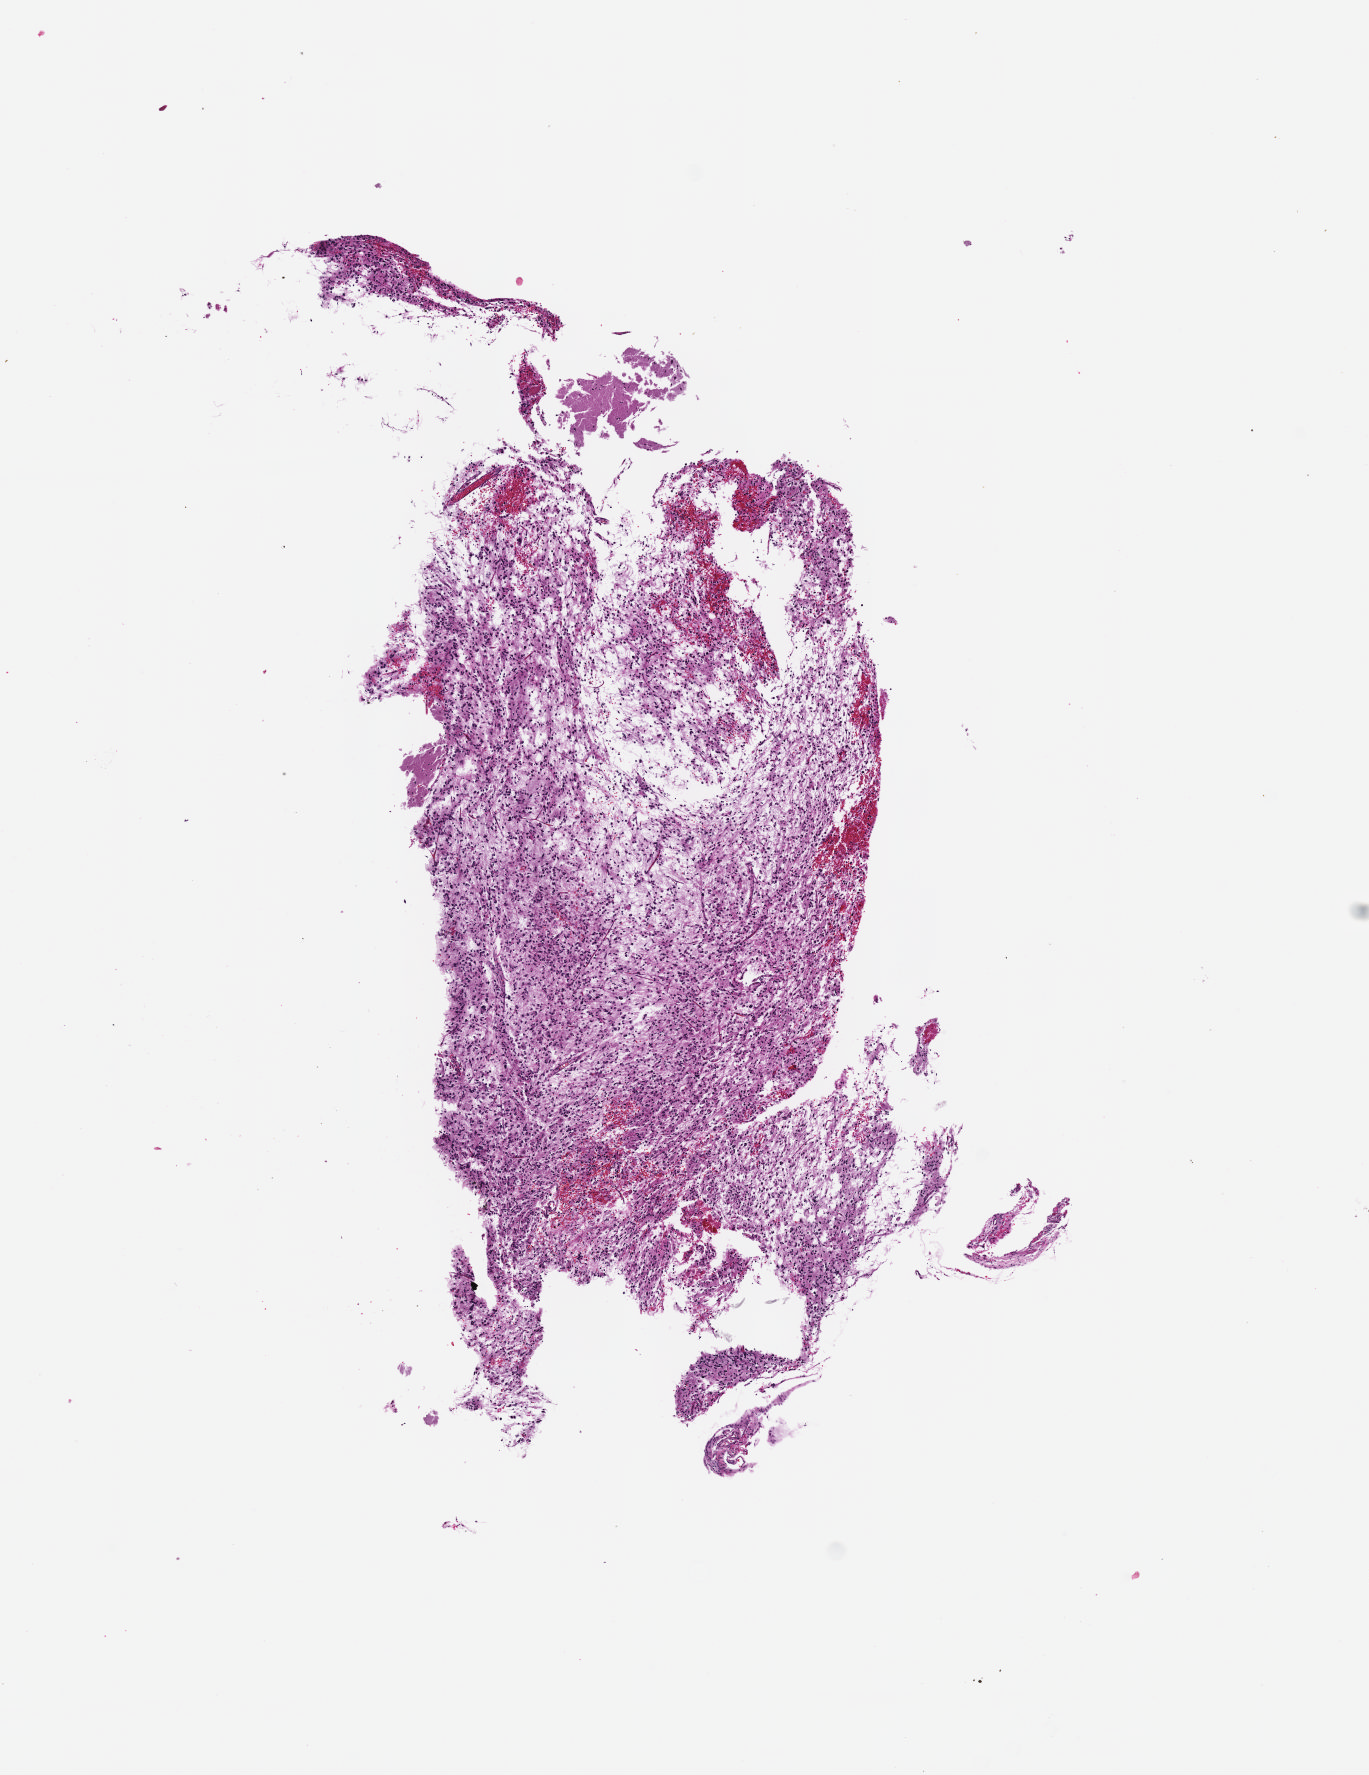
H&E-stained whole-slide image — low-resolution overview of the scanned area, about 5.5 x 7.2 mm (from a 40x scan). FFPE section. Sample: primary tumour, brain. Male, age 36 years at initial diagnosis. Histologic grade: G2 (moderately differentiated).
• diagnosis: Astrocytoma, NOS (cerebrum)